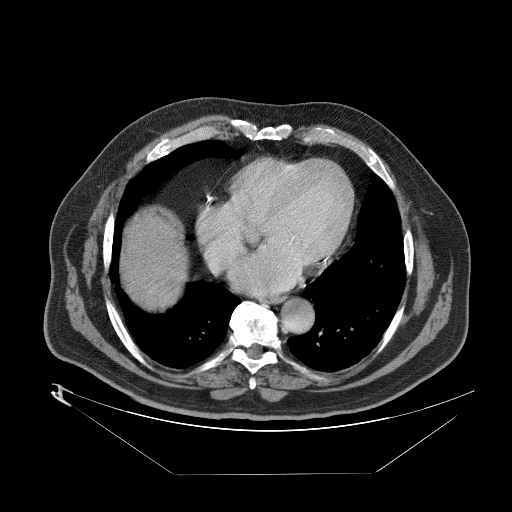
Contrast-enhanced abdominal CT (liver protocol), one axial slice; slice 83 of 89 in the series (ordered by position); 140 kVp; one of 2 acquisitions stored at this slice position; soft-tissue window (W 400 / L 40 HU); 2.5 mm slice thickness; 512 × 512 image matrix. From the clinical record (not read from this slice): diagnosis: hepatocellular carcinoma (patient treated with transarterial chemoembolisation; whether this scan precedes or follows treatment is not stated here); TNM stage (as recorded): Stage-II; Child-Pugh class: B; tumour differentiation: moderately differentiated; tumour nodularity: multinodular.
Annotated regions visible in this slice (semi-automatically segmented with operator editing):
- abdominal aorta: bounding box <277,297,312,332> (left, top, right, bottom; pixels)
- liver parenchyma outside the tumour (the mass and vessels are separate outlines, so this box may not span the whole liver): <126,222,176,276>
- liver vessels: <131,227,176,236>